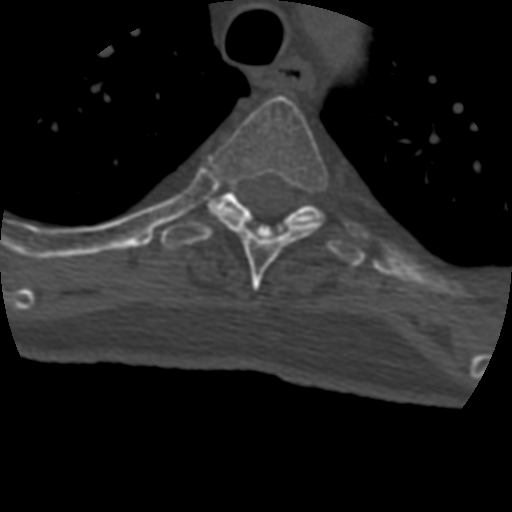
CT including the spine, one axial slice; slice 331 of 399 in the series (ordered by position); reconstruction kernel STANDARD; 120 kVp; bone window (W 1800 / L 400 HU); 1.25 mm slice thickness; 512 × 512 image matrix, field of view 160 × 160 mm. Patient age 69 years. From the clinical record (not read from this slice): primary cancer: prostate.
Annotated regions visible in this slice (semi-automatic segmentation, software-assisted and operator-edited):
- T4 vertebra: box from (x=207, y=96) to (x=329, y=291) px
- T5 vertebra: (x=160, y=186)–(x=366, y=267)